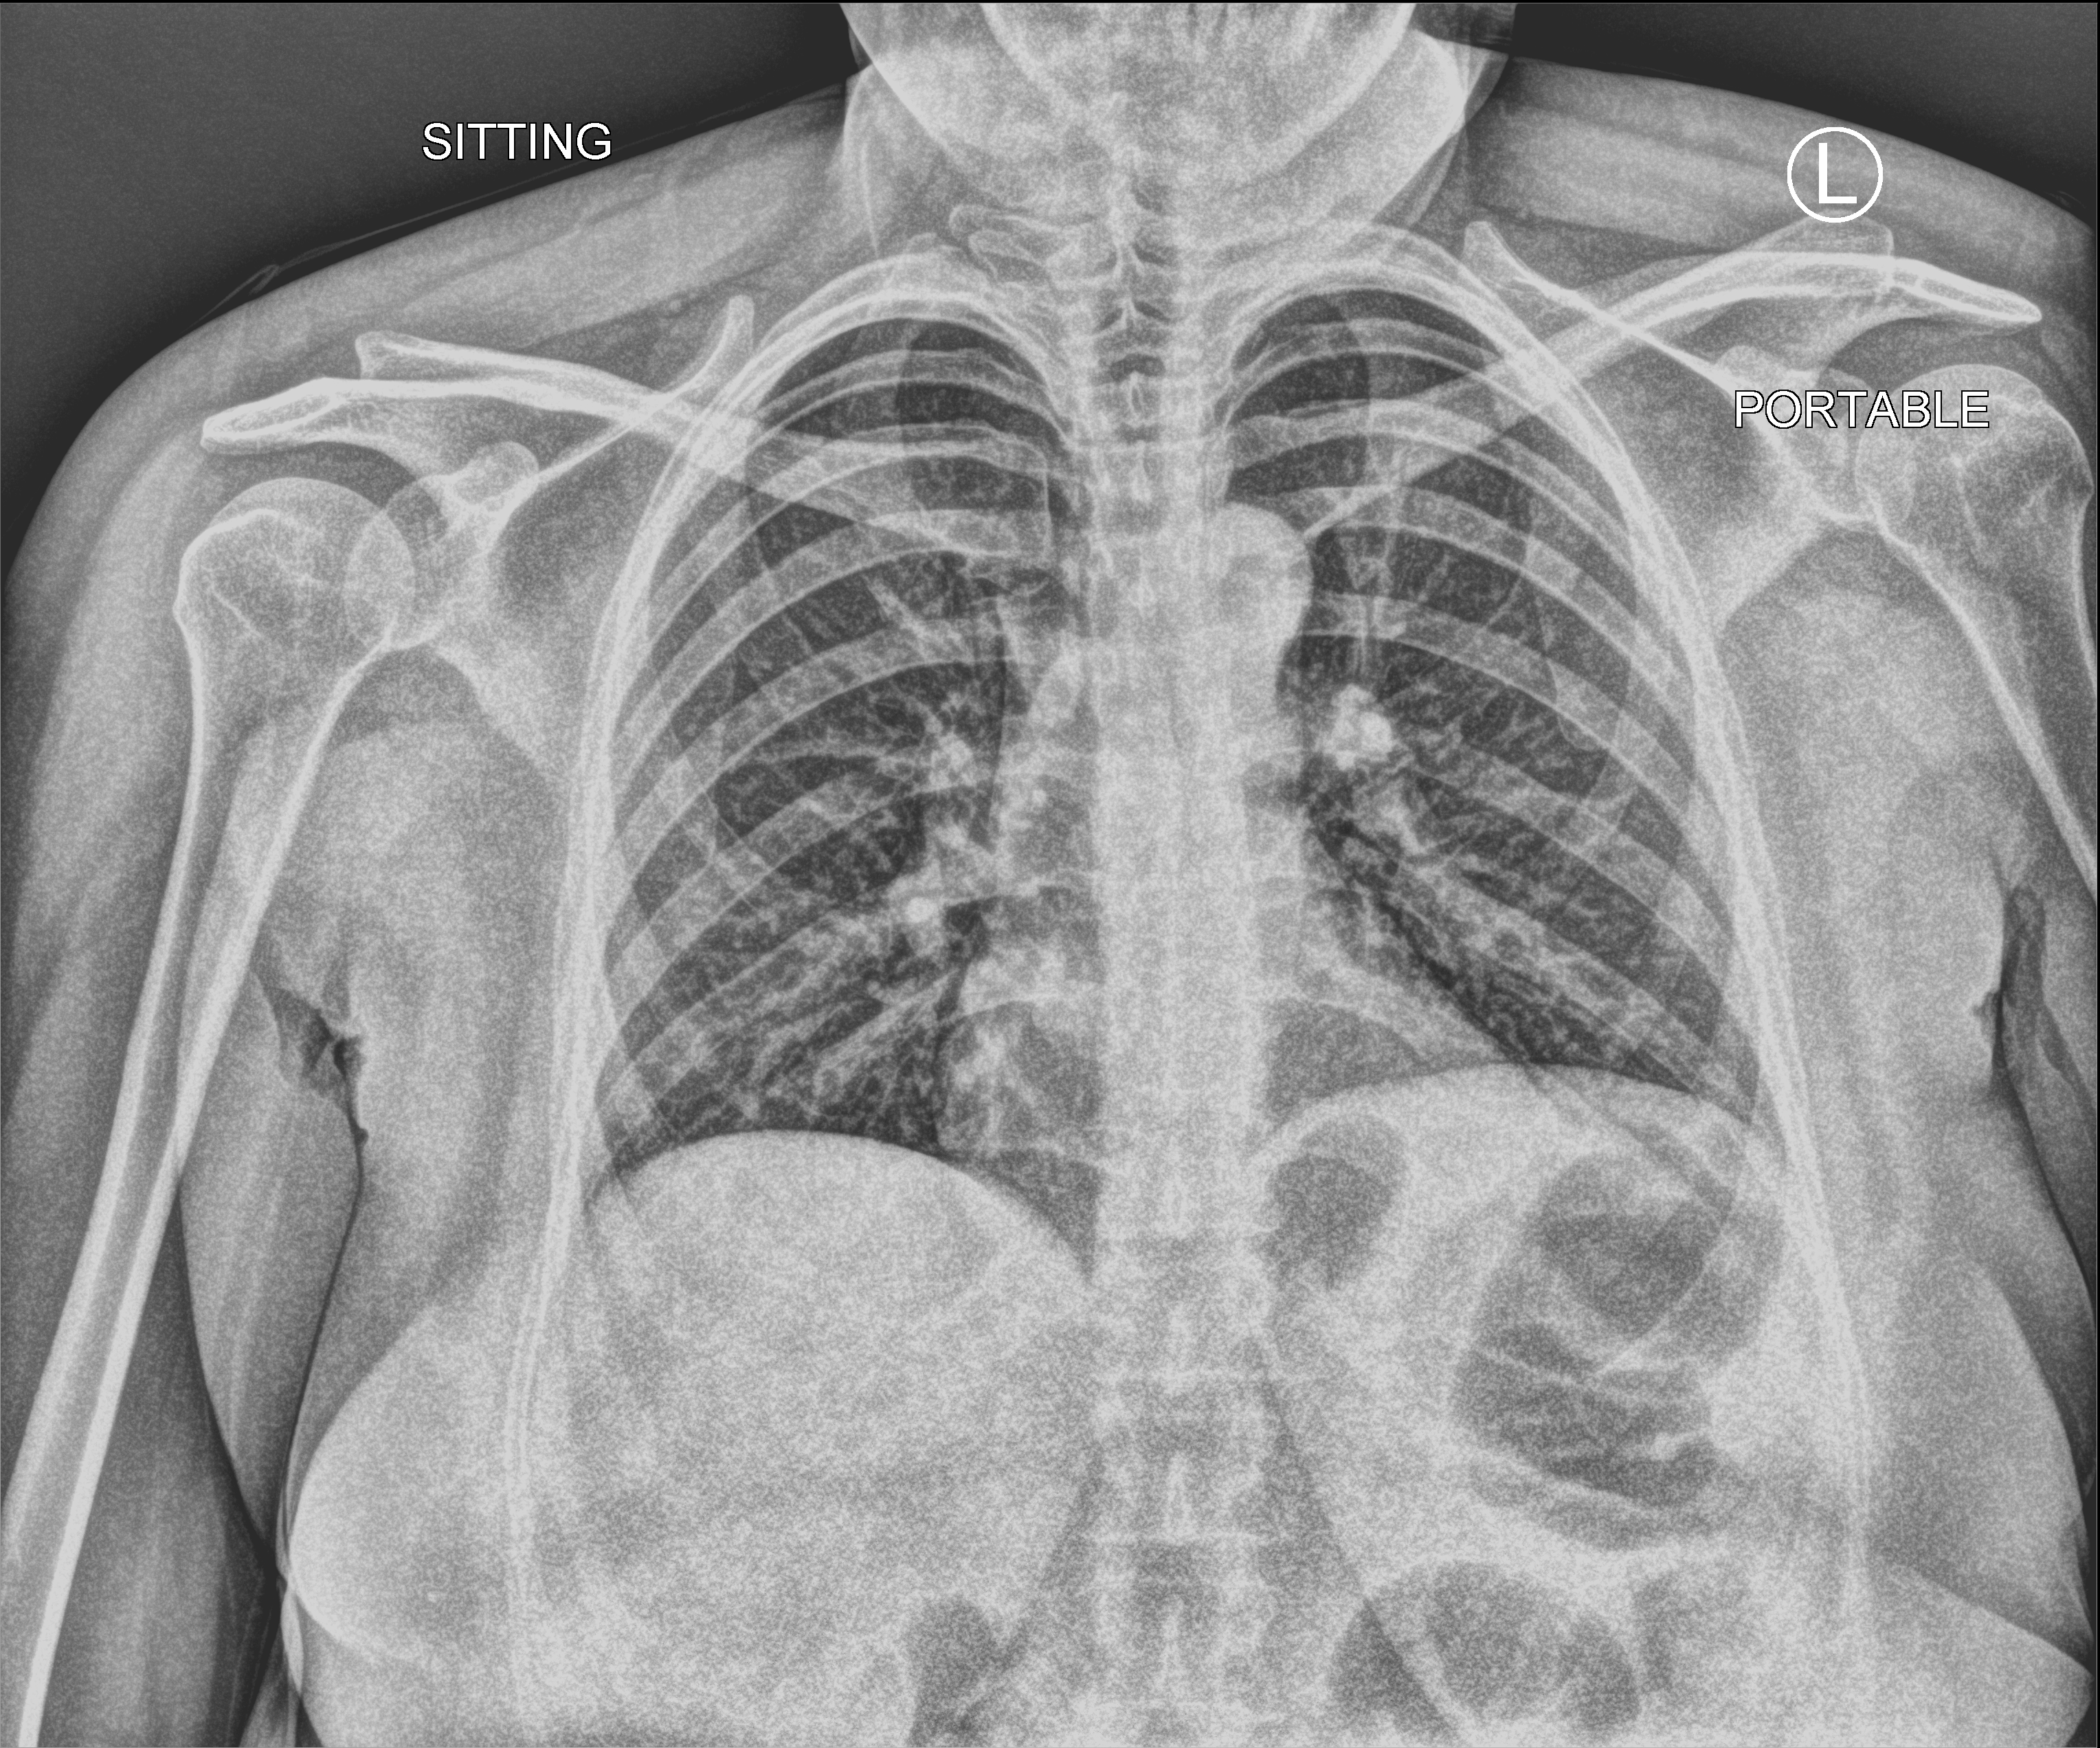
Chest X-ray (portable), anteroposterior (AP) projection. Female patient hospitalised with COVID-19, age 18–59 years.
From the hospital-stay record, not from the radiograph (when in the stay this image was taken is not recorded):
- admitted to intensive care during this hospital stay: no
- mechanically ventilated during this hospital stay: no
- smoking status (admission record): never